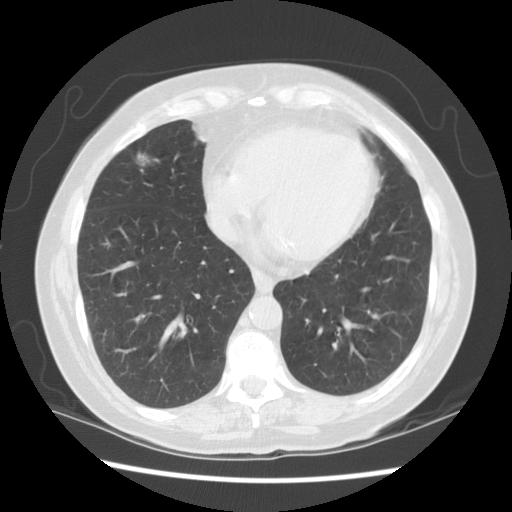
Axial slice from a low-dose chest CT screening exam, second screening round (one year after baseline), lung window (W 1500 / L -600 HU), 2.5 mm slice thickness, standard (soft-tissue) reconstruction kernel (STANDARD), 140 kVp, slice 43 of 115 in the series, 512 × 512 image matrix, field of view 340 × 340 mm. Female, age 71 years at enrolment. Current smoker at enrolment.
- Expert-annotated lung lesion, bounding box <100,137,169,189> (left, top, right, bottom; pixels).
- Reader record for this screening exam (exam-level; its link to the box is not recorded): non-calcified nodule or mass ≥4 mm, right middle lobe, 6 × 6 mm, spiculated (stellate) margins, soft tissue attenuation, pre-existing on the prior screen: yes; interval growth: yes.
- Official screen result: positive, other.
- Later outcome: lung cancer diagnosed 68 days after this screen — adenocarcinoma, NOS, right middle lobe, moderately differentiated (G2), stage IA (AJCC 6th edition), 12 mm at pathology.